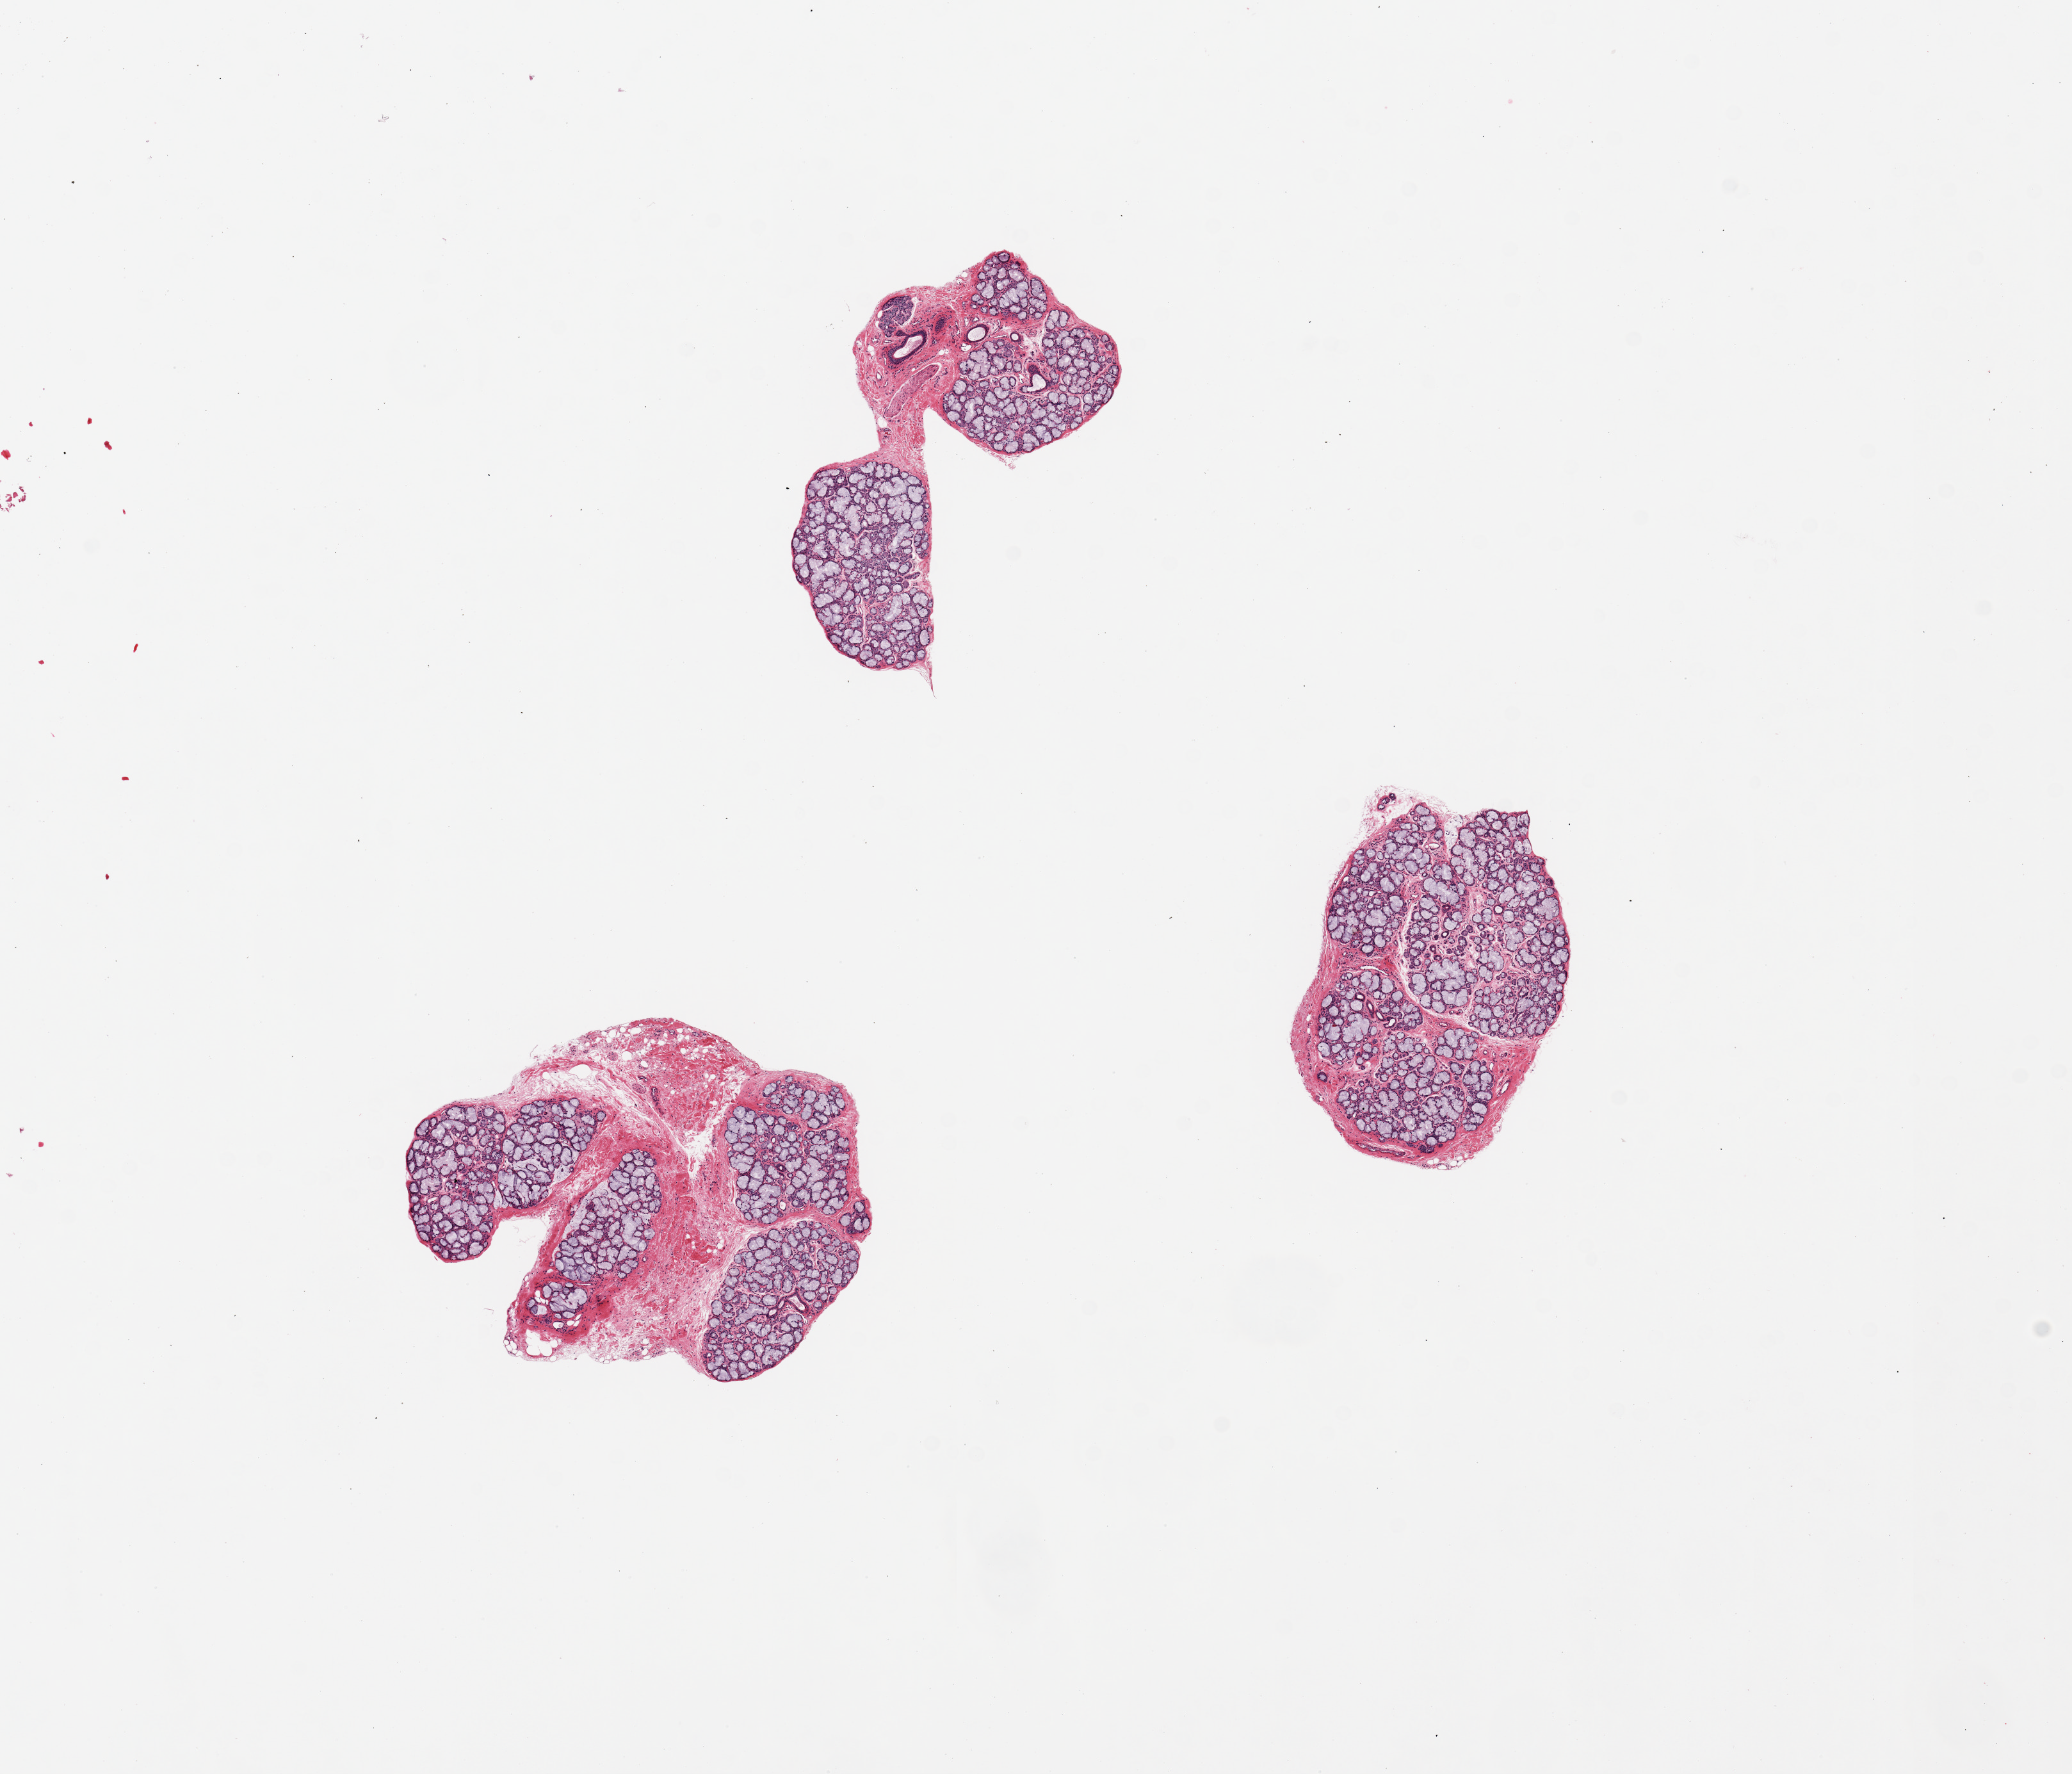
Whole-slide image, H&E stain, brightfield — whole scanned area (about 12.8 x 11.0 mm, from a 20x scan) shown as a low-resolution overview, PAXgene-fixed, paraffin-embedded tissue, sampled site (target tissue): minor salivary gland, donor tissue sample. Donor: male.
Review note (as recorded): 3 pieces, ~80% glandular tissue, good specimens.